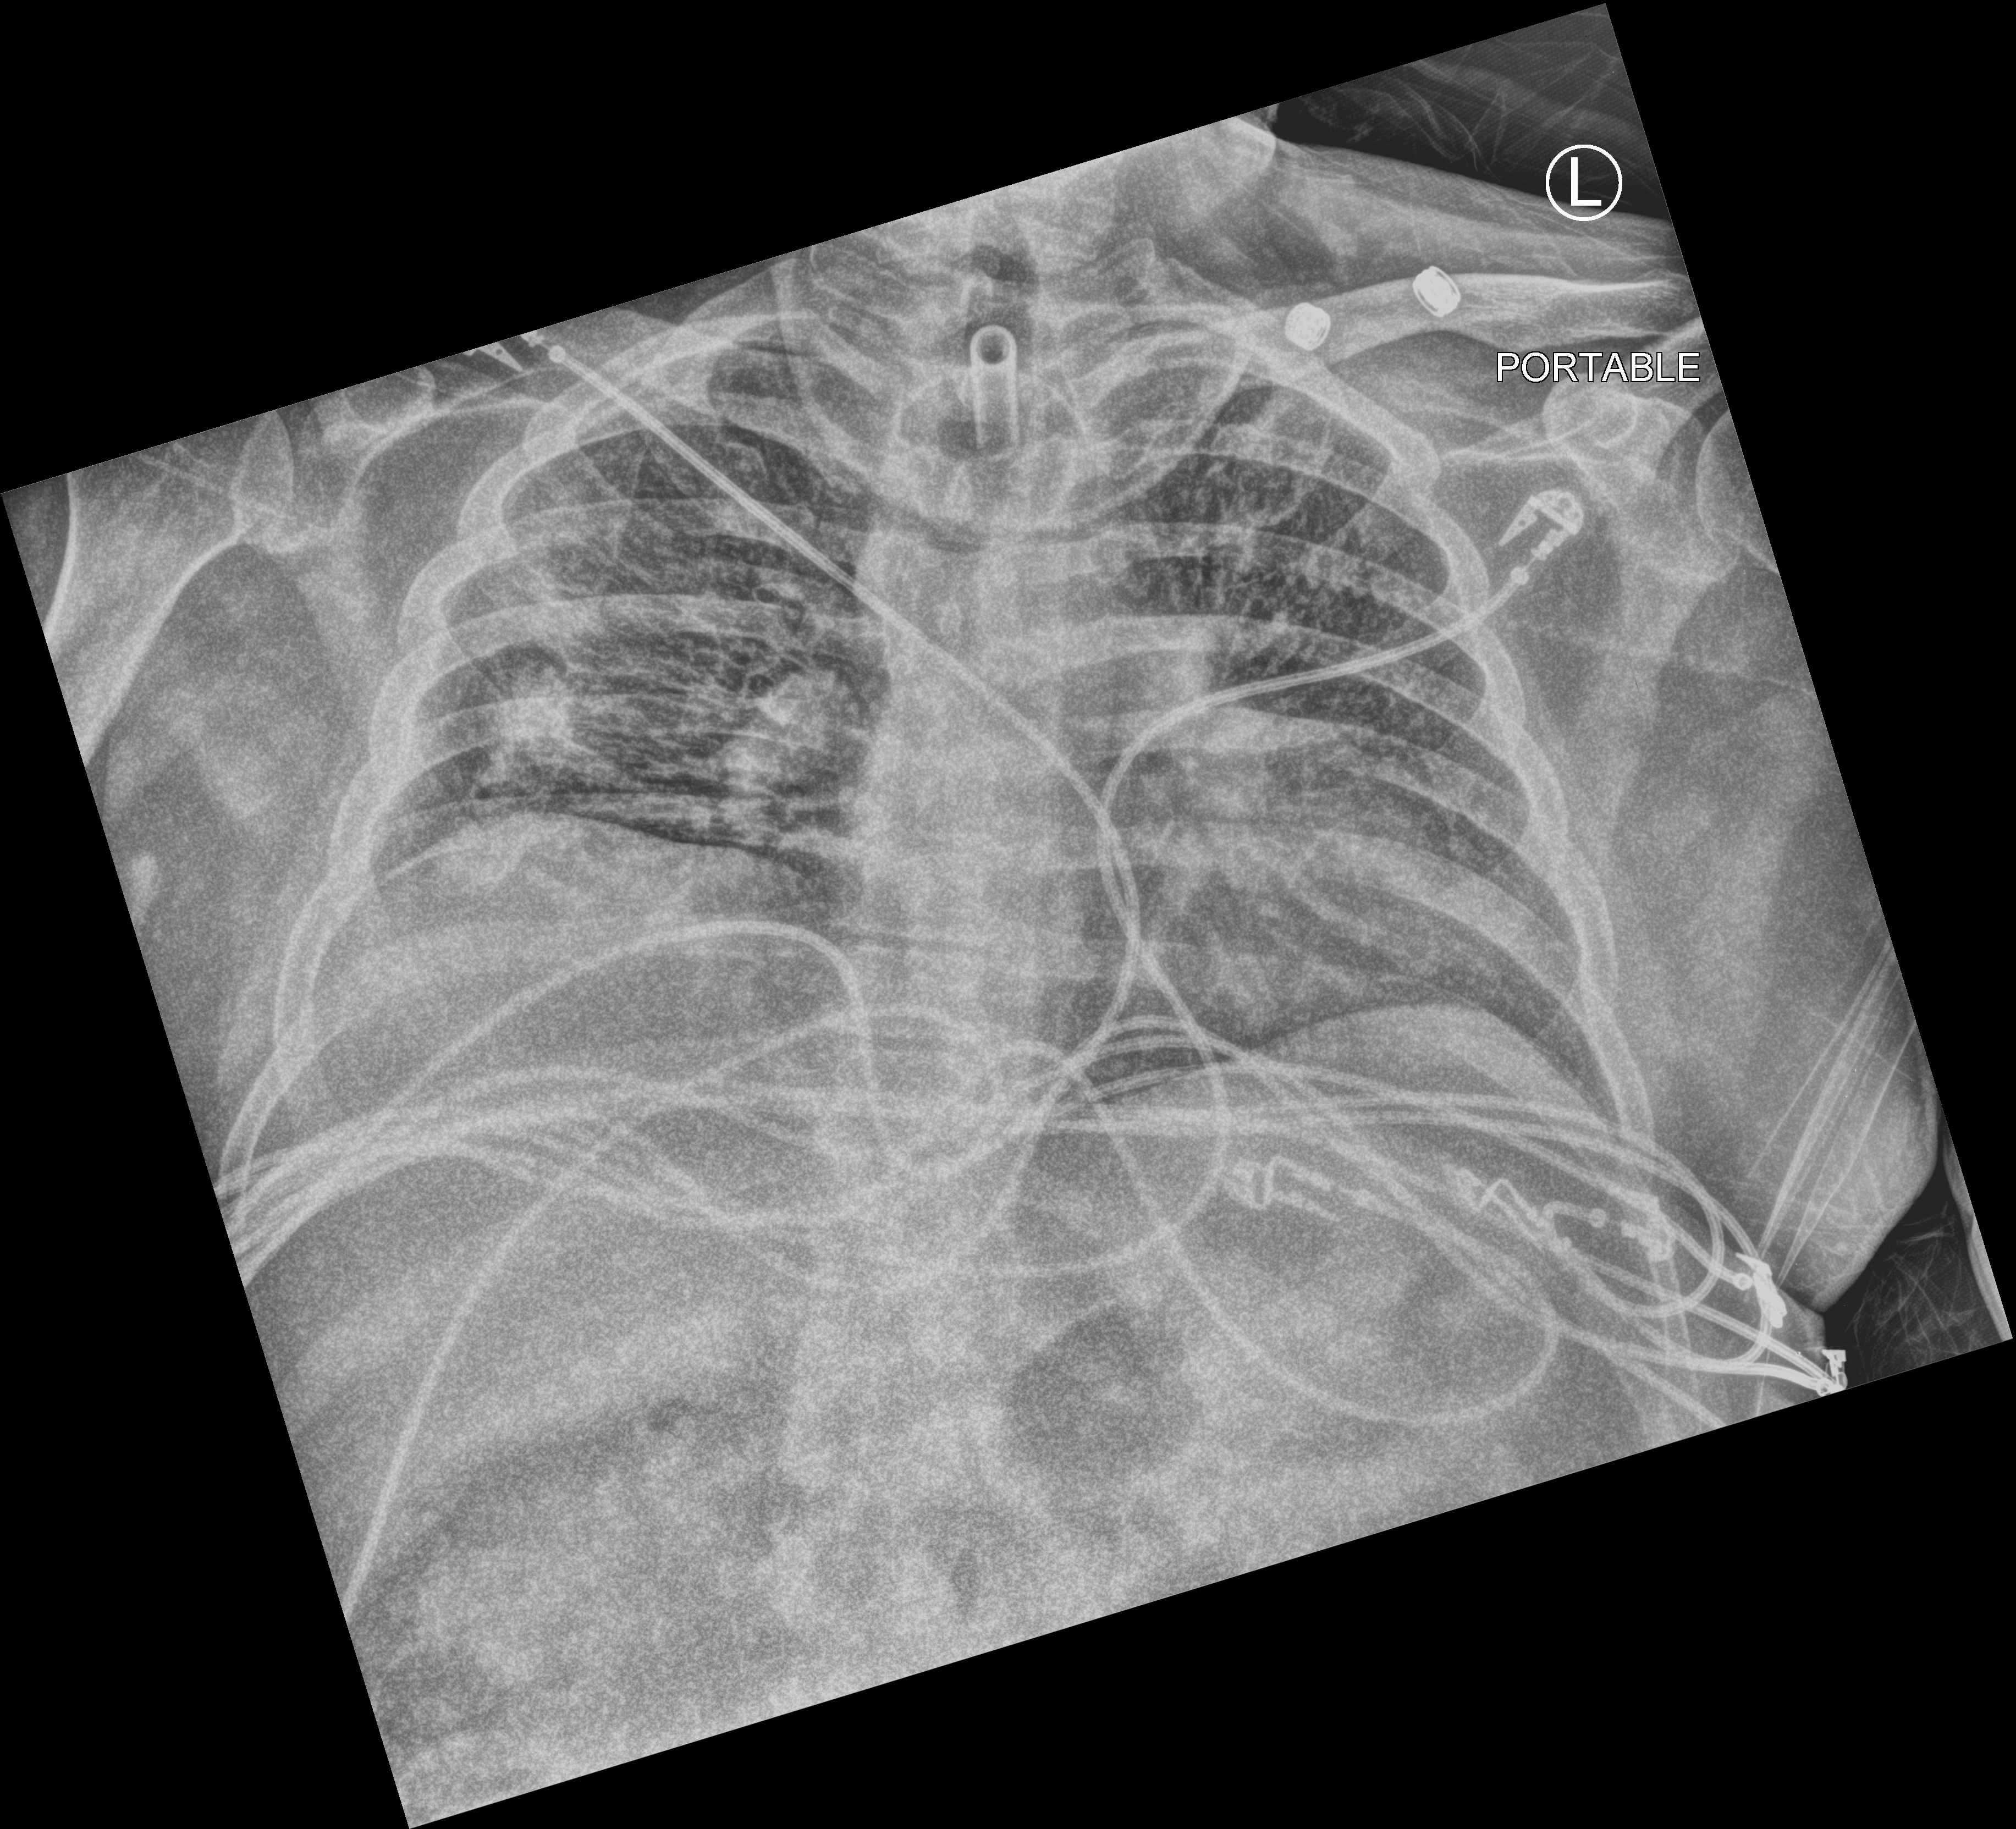
Portable chest radiograph; anteroposterior (AP) projection. Patient hospitalised with COVID-19; male, aged 18–59 years.
From the hospital-stay record, not from the radiograph (when in the stay this image was taken is not recorded): mechanically ventilated during this hospital stay: yes; other chronic lung disease (admission record): no; diabetes (admission record): no.